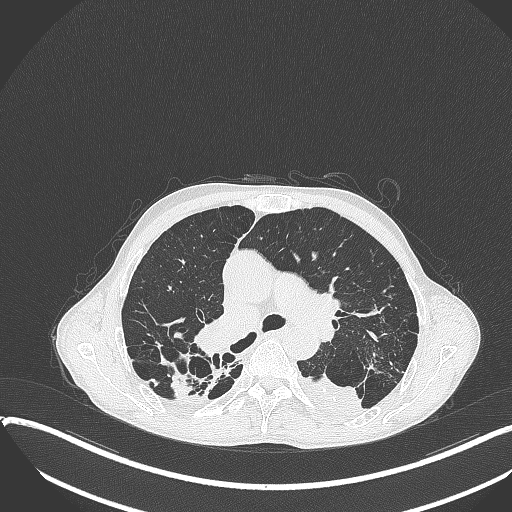
Chest CT, one axial slice; slice 246 of 401 in the series (ordered by position); 120 kVp; lung window (W 1500 / L -600 HU); 512 × 512 image matrix, field of view 400 × 400 mm. Male patient, age 57 years. Case-level facts recorded for this patient, not image findings: clinical TNM (as recorded): T4 N0 M0.
Structures marked on this image (bounding box drawn by a radiologist):
- lung tumour (recorded histology: squamous cell carcinoma): bounding box (x1, y1, x2, y2) in pixels: (300, 370, 365, 423)